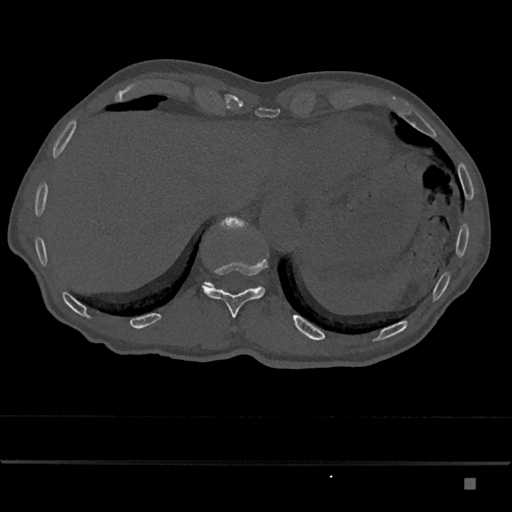
CT including the spine, one axial slice. 120 kVp. Bone window (W 1800 / L 400 HU). 0.5 mm slice thickness. 512 × 512 image matrix, field of view 390 × 390 mm. Patient: male, 72 years. Case-level facts recorded for this patient, not image findings: primary cancer: prostate.
Annotated regions visible in this slice (semi-automatically segmented with operator editing):
- T11 vertebra: bounding box <202,259,267,318> (left, top, right, bottom; pixels)
- T12 vertebra: <204,216,260,288>